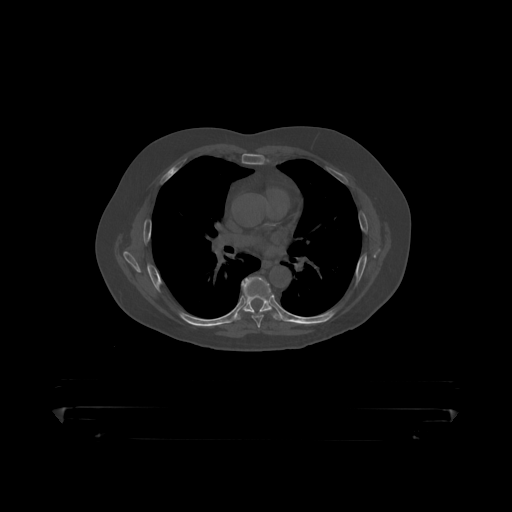
CT including the spine, one axial slice; position 289 of 390 along the scan axis; reconstruction kernel STANDARD; 120 kVp; bone window (W 1800 / L 400 HU); 512 × 512 image matrix. Patient: male, 60 years. Case-level facts recorded for this patient, not image findings: primary cancer: prostate.
Outlined on this slice (semi-automatically segmented with operator editing):
- T6 vertebra: box from (x=242, y=277) to (x=269, y=319) px
- T7 vertebra: (x=240, y=277)–(x=280, y=317)